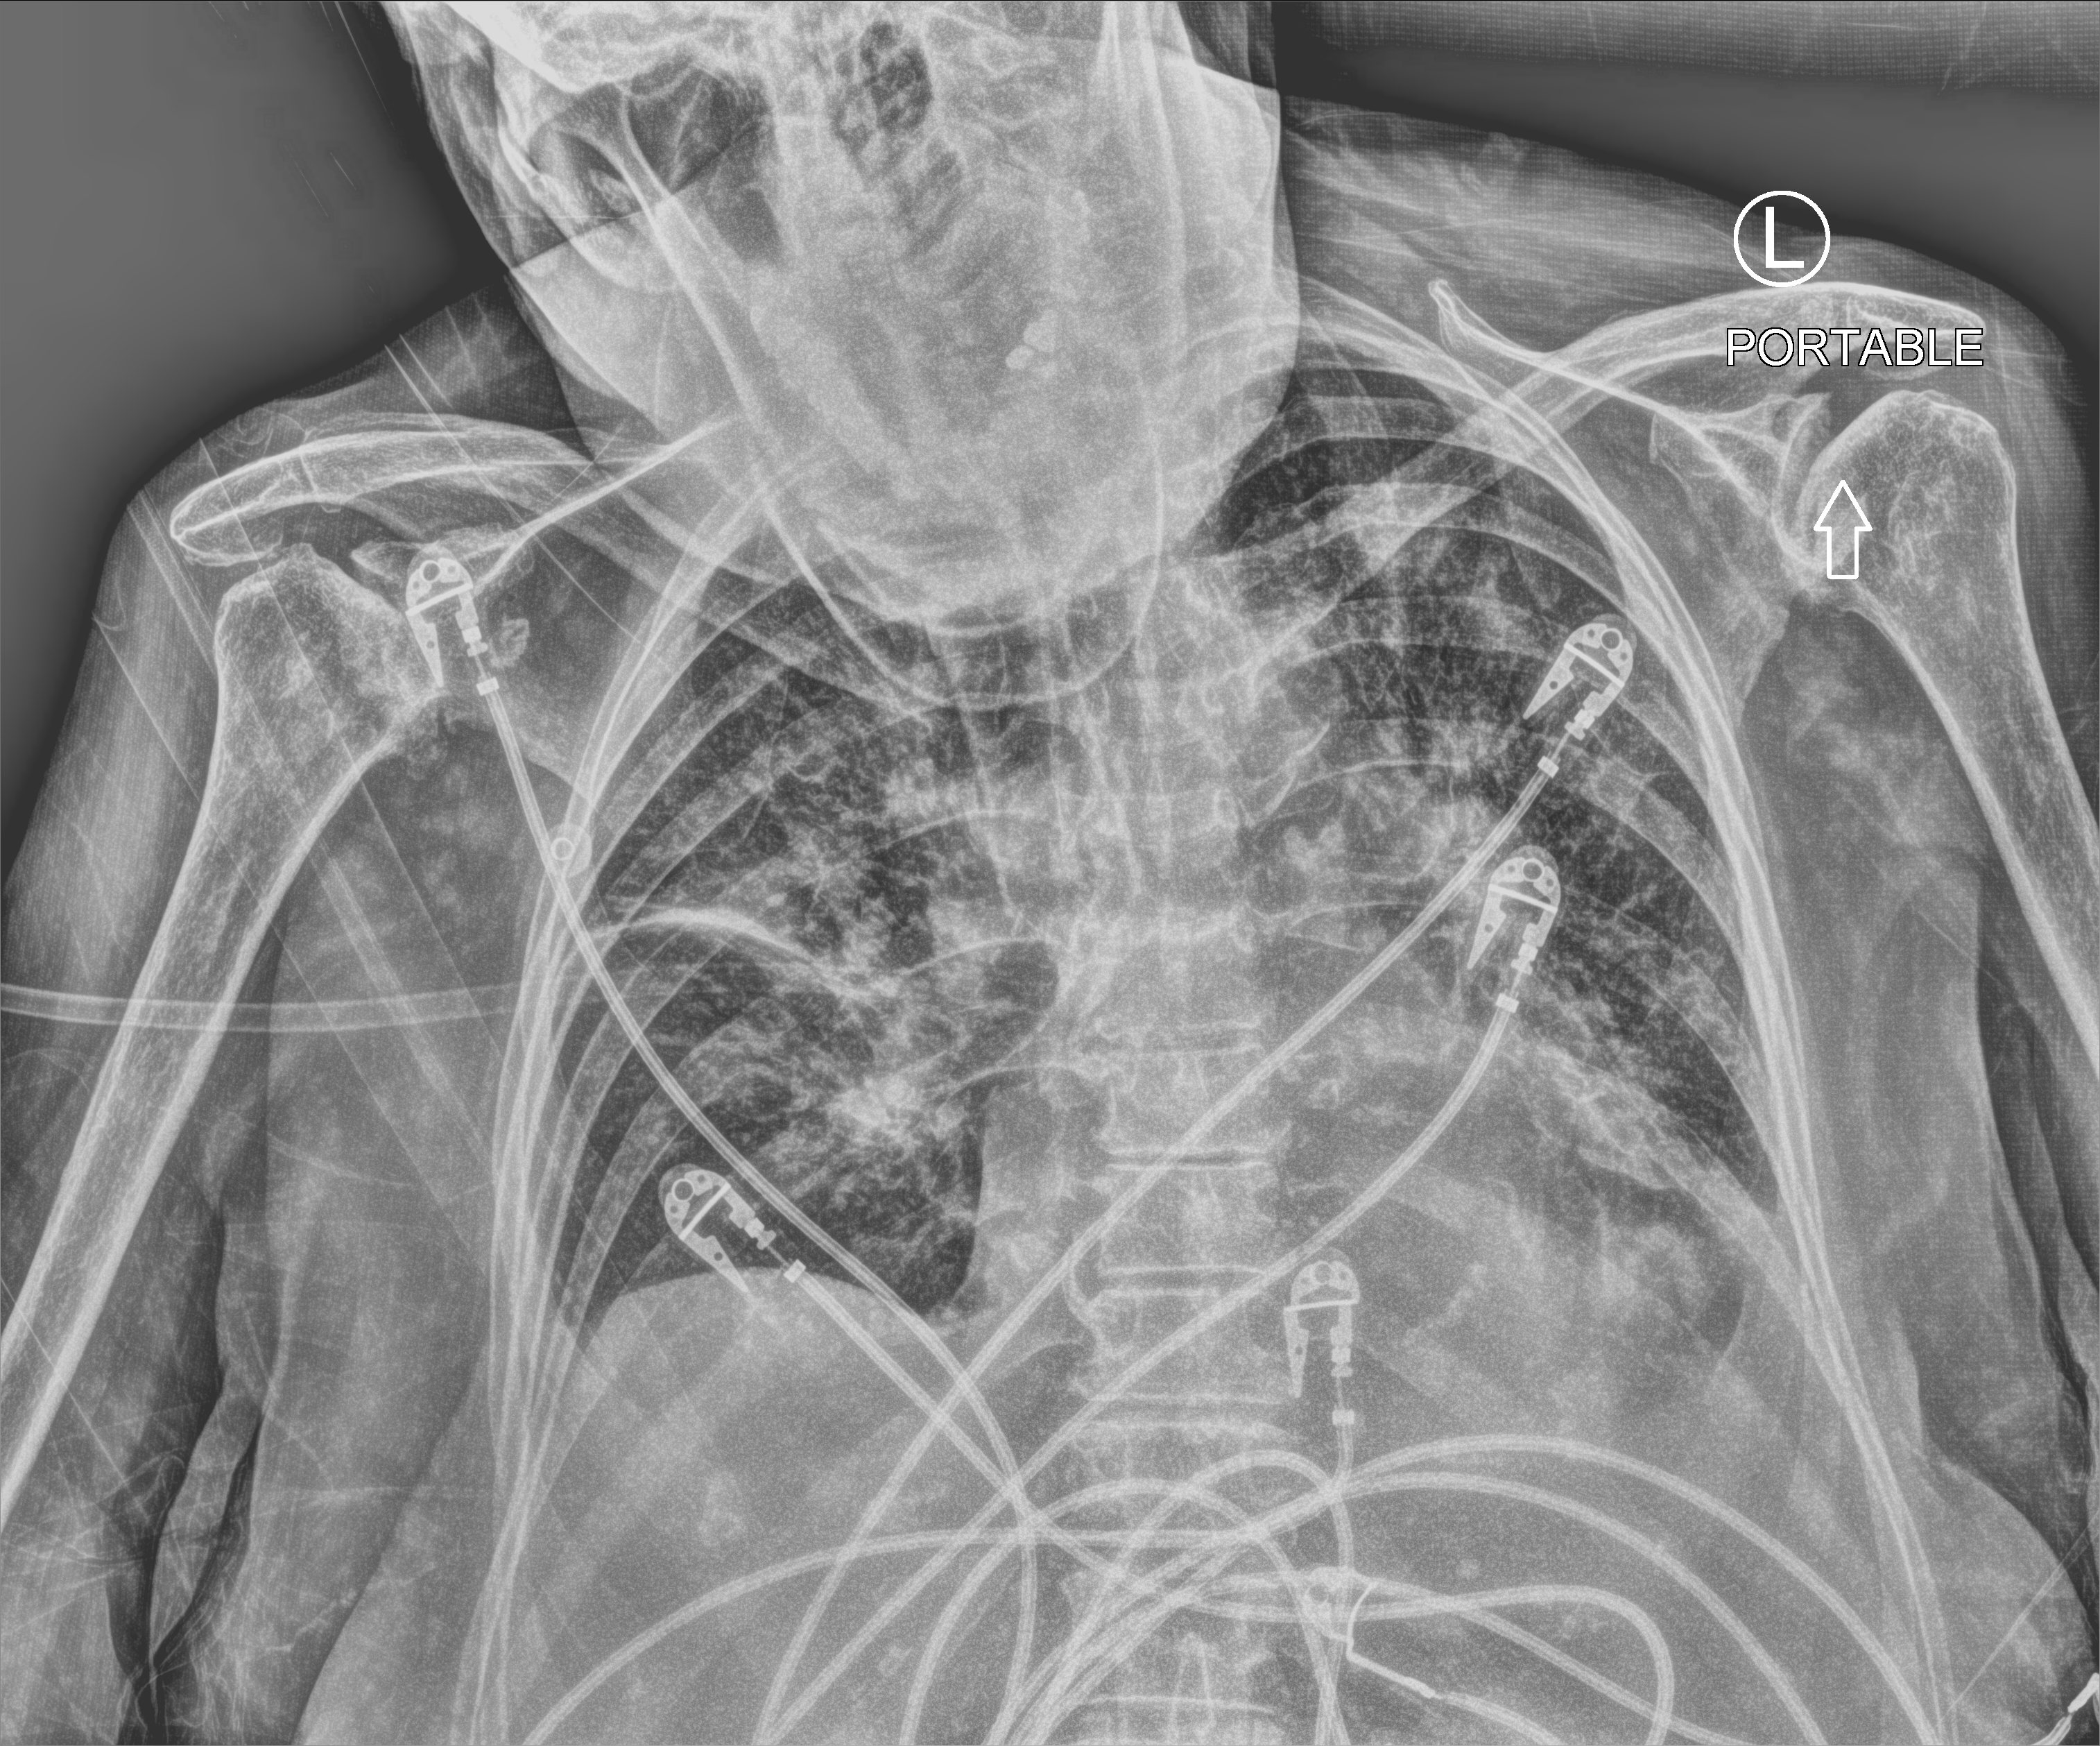
Chest X-ray (portable); anteroposterior (AP) projection. Female patient hospitalised with COVID-19, age 75–90 years.
Hospital-stay facts (about this admission, not read from this image; timing relative to this image not recorded): admitted to intensive care during this hospital stay: no; mechanically ventilated during this hospital stay: no.